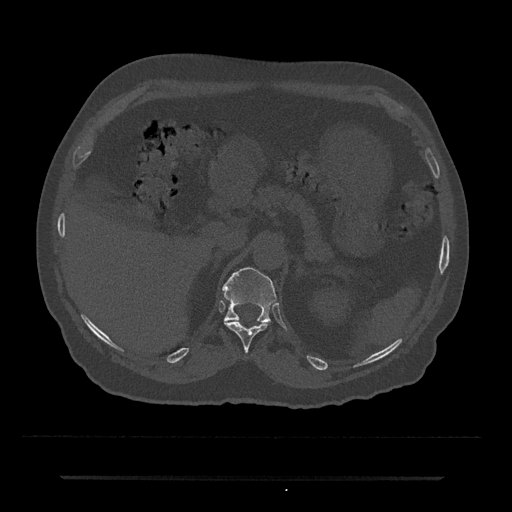
CT including the spine, one axial slice. Position 156 of 797 along the scan axis. Reconstruction kernel Br40s/3. 120 kVp. Bone window (W 1800 / L 400 HU). 0.5 mm slice thickness. 512 × 512 image matrix. Male patient, age 69 years. Case-level facts recorded for this patient, not image findings: primary cancer: prostate.
Outlined on this slice (semi-automatic segmentation, software-assisted and operator-edited):
- T11 vertebra: box from (x=224, y=321) to (x=267, y=351) px
- T12 vertebra: (x=222, y=267)–(x=276, y=322)